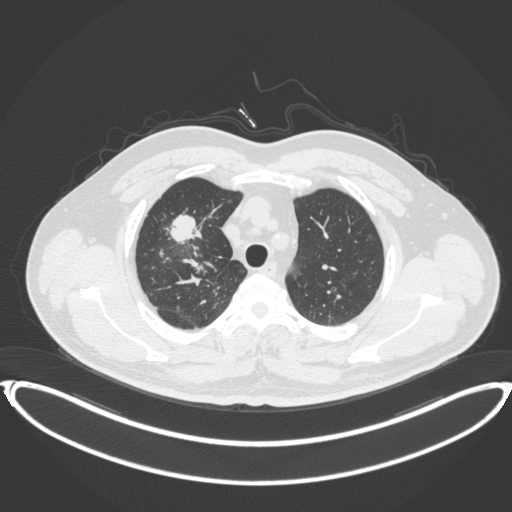
Chest CT, one axial slice. Slice 307 of 399 in the series (ordered by position). 120 kVp. Lung window (W 1500 / L -600 HU). 1 mm slice thickness. 512 × 512 image matrix. Male patient, age 53 years. Case-level facts recorded for this patient, not image findings: clinical TNM (as recorded): T2a N0 M0.
Annotated regions visible in this slice (bounding box drawn by a radiologist):
- lung tumour (recorded histology: adenocarcinoma): bounding box <163,213,204,246> (left, top, right, bottom; pixels)